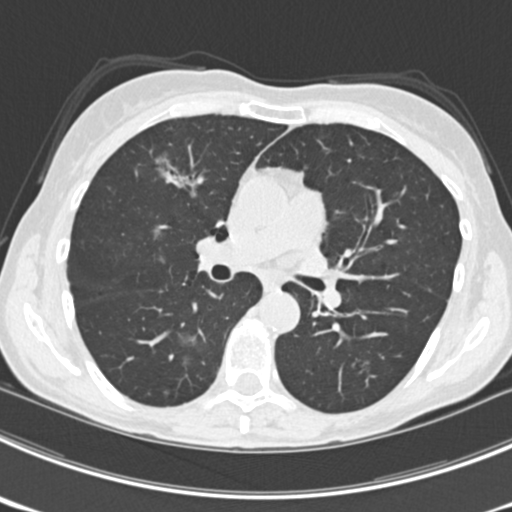
Chest CT (low-dose screening protocol), one axial image; third screening round (two years after baseline); lung window (W 1500 / L -600 HU); 2 mm slice thickness; standard (soft-tissue) reconstruction kernel (B30f); 512 × 512 image matrix. Female, age 63 years at enrolment. Current smoker at enrolment.
Expert-annotated lung lesion, bounding box [x1, y1, x2, y2] px = [149, 145, 212, 202]. The screening reader recorded 9 non-calcified nodules or masses ≥4 mm on this exam; which of them this box marks is not recorded. Official screen result: positive, other. Later outcome: lung cancer diagnosed 15 days after this screen — bronchiolo-alveolar adenocarcinoma, NOS, right upper lobe, right middle lobe, right lower lobe, left upper lobe, left lower lobe, moderately differentiated (G2), stage IV (AJCC 6th edition).